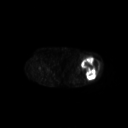
FDG PET of an extremity soft-tissue mass (from a PET/CT study), one axial slice; position 226 of 267 along the scan axis; 3.27 mm slice thickness; 128 × 128 image matrix, field of view 700 × 700 mm. Patient: female, 62 years. Case-level facts recorded for this patient, not image findings: histological type: undifferentiated – high grade; grade: high; site of the primary tumour: left thigh.
Annotated regions visible in this slice (expert contour drawn on MRI and transferred to this co-registered scan by the dataset authors):
- gross tumour volume including surrounding oedema: bounding box <81,56,100,79> (left, top, right, bottom; pixels)
- gross tumour volume (mass): <81,56,99,79>